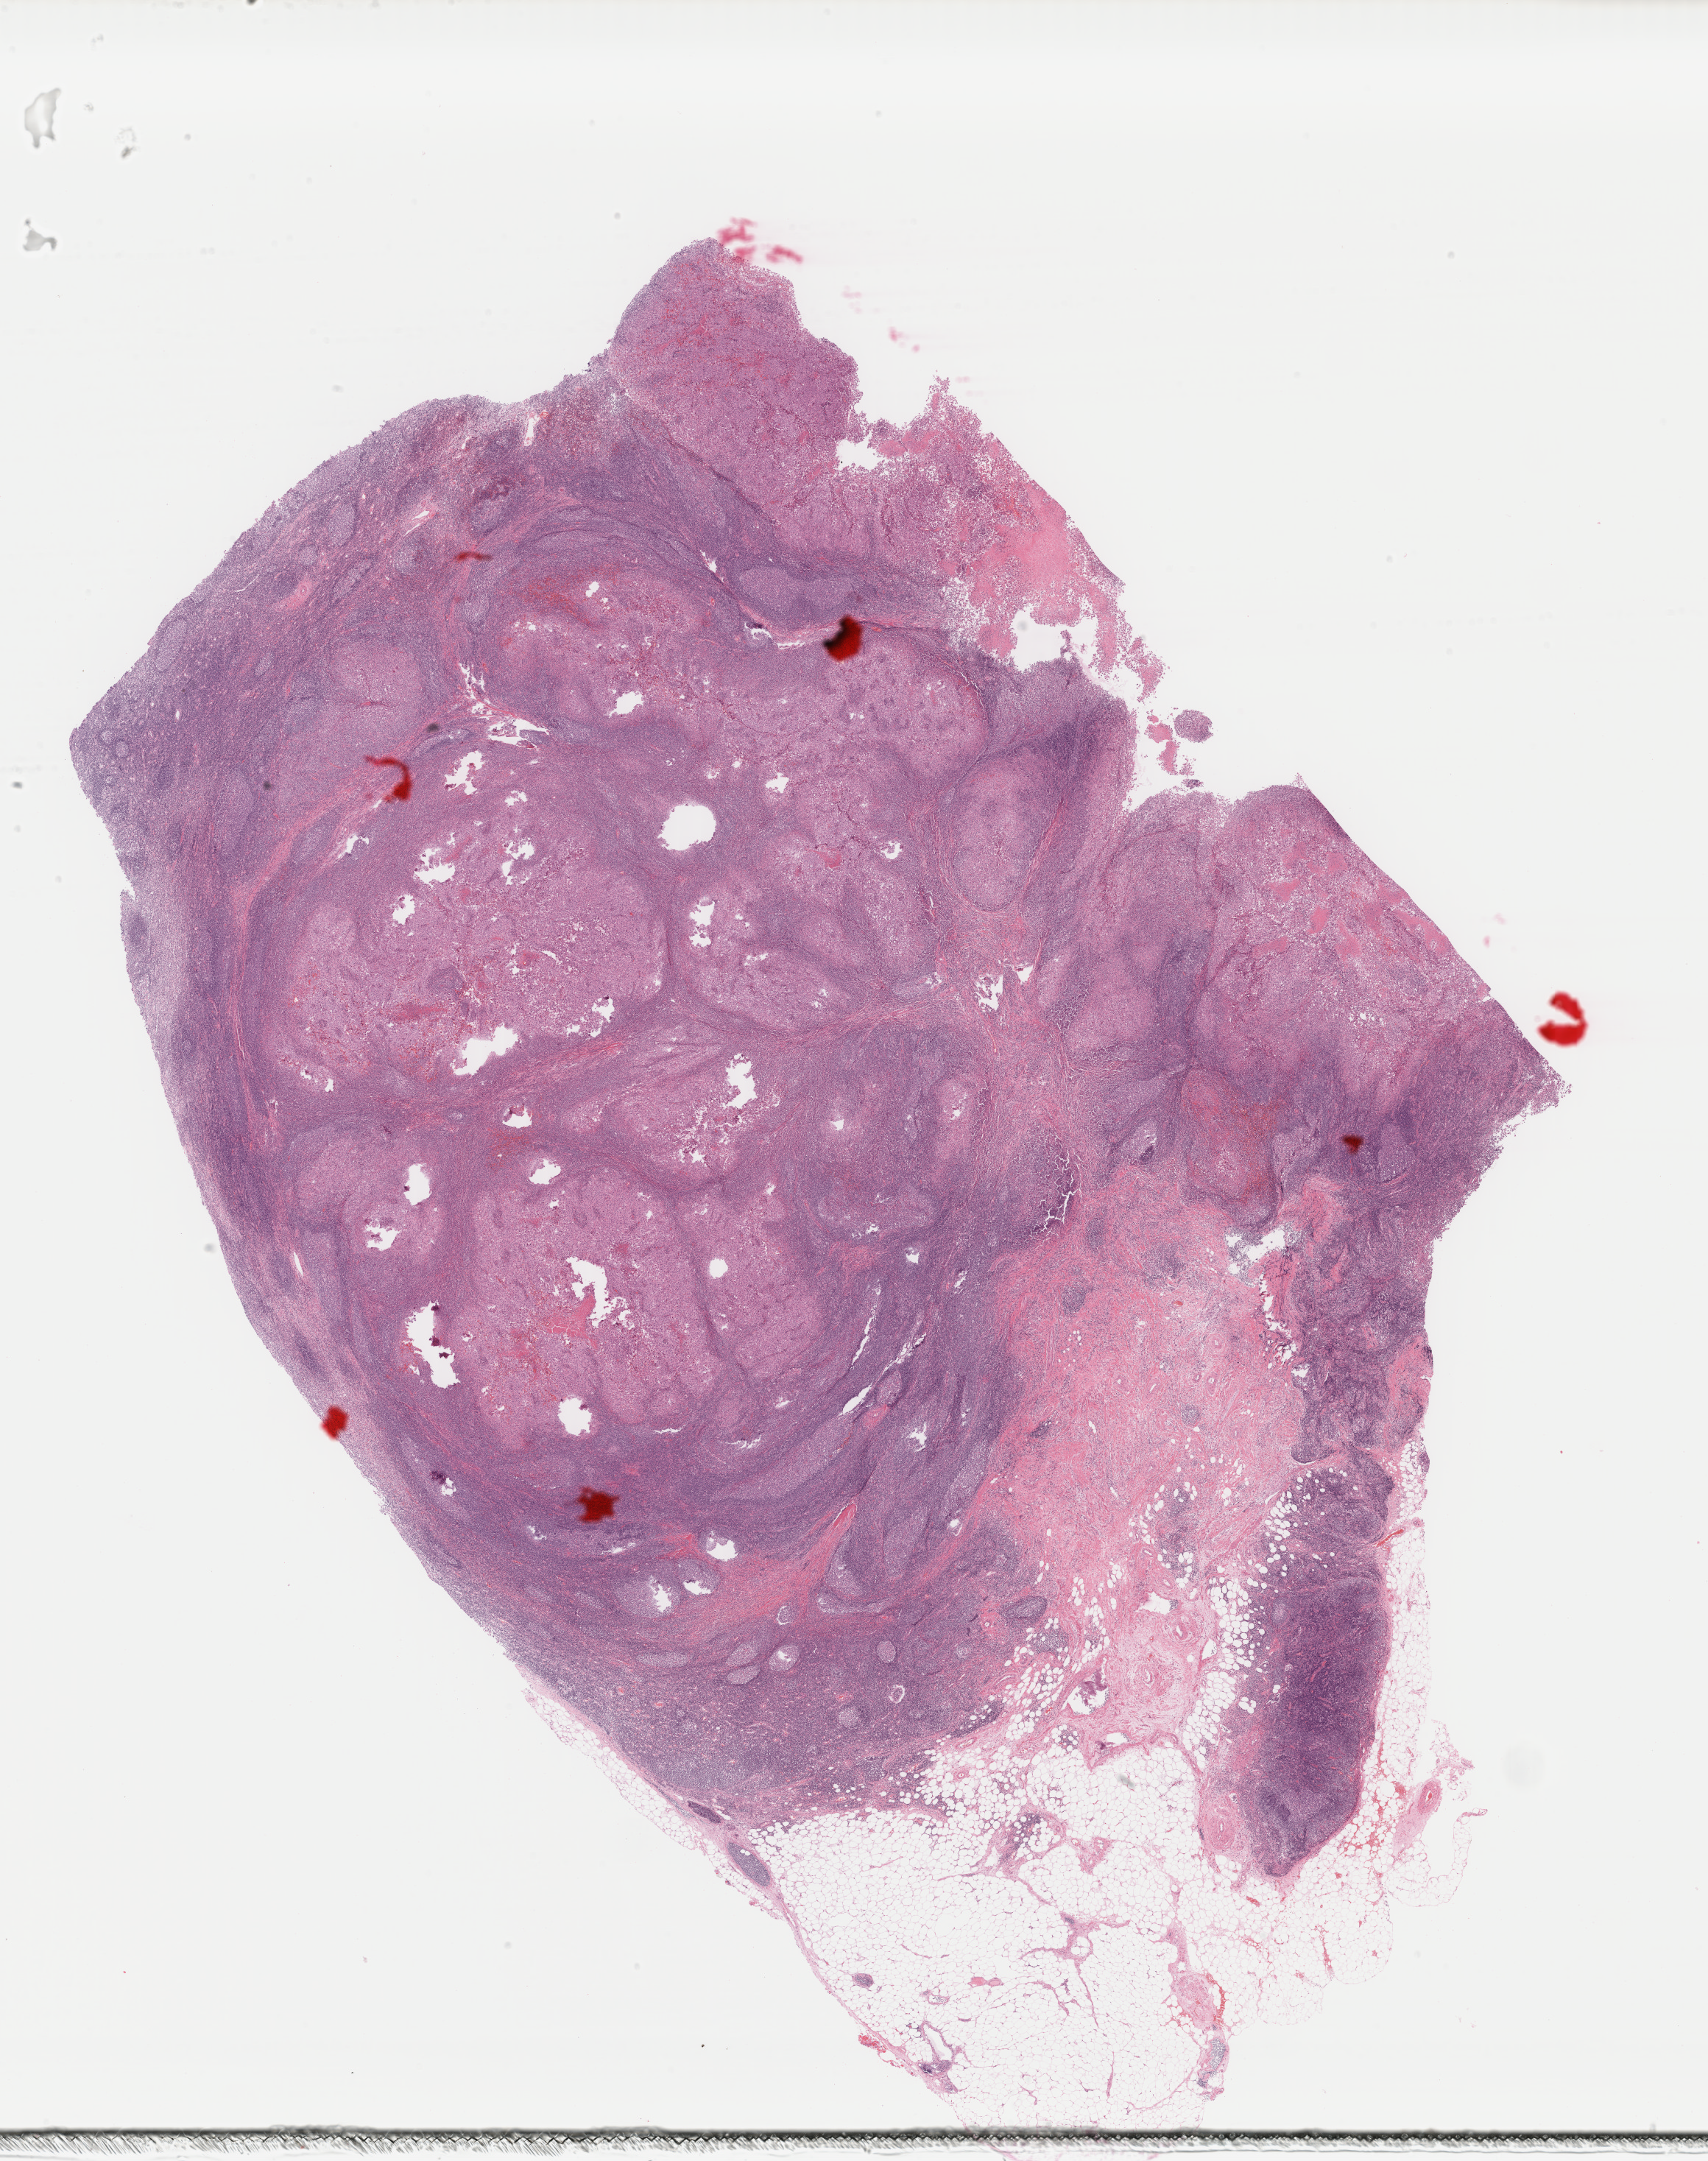
Whole-slide histology image, H&E-stained, shown as a low-resolution overview of the whole scanned area (about 18.4 x 23.3 mm, acquisition: 40x scan); FFPE section; metastatic tumour sample, sampled site: lymph nodes of inguinal region or leg. Patient: female, age at initial diagnosis 74 years.
• this section: metastatic tumour tissue
• patient diagnosis: Malignant melanoma, NOS